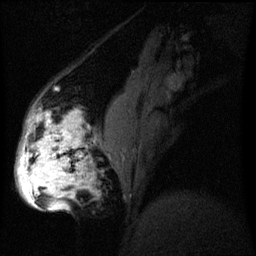
Breast MRI (dynamic contrast-enhanced), one sagittal slice; dynamic contrast-enhanced series, image 2 of 3 at this slice position (ordered by acquisition); 1.5 T; TE 4.2 ms, TR 8 ms; 2.2 mm slice thickness; 256 × 256 image matrix. Patient: female, 50 years.
Outlined on this slice (semi-automatically segmented with operator editing):
- analysis volume of interest (the breast-tissue region the enhancement analysis was run in; not a lesion): box from (x=19, y=112) to (x=92, y=211) px
- tumour enhancement mask (voxels above the 70 % enhancement threshold inside the analysis volume of interest): (x=19, y=116)–(x=82, y=211)